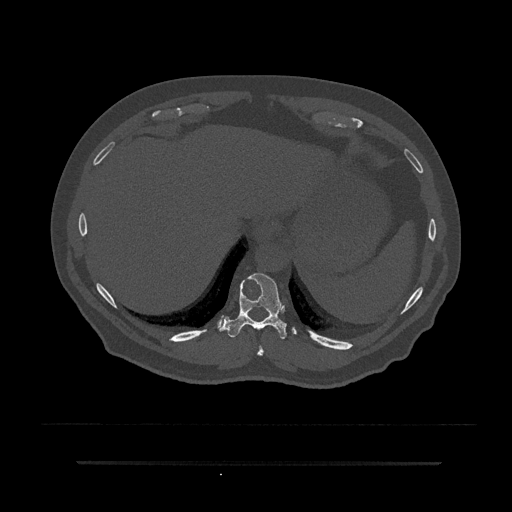
CT including the spine, one axial slice; position 330 of 797 along the scan axis; bone window (W 1800 / L 400 HU); 0.5 mm slice thickness; 512 × 512 image matrix, field of view 464 × 464 mm. Patient: male, 59 years. From the clinical record (not read from this slice): primary cancer: bile ducts; vertebrae with lytic lesions (as recorded): T10.
Structures marked on this image (semi-automatically segmented with operator editing):
- T10 vertebra: box from (x=221, y=273) to (x=297, y=339) px
- T9 vertebra: (x=257, y=345)–(x=264, y=356)